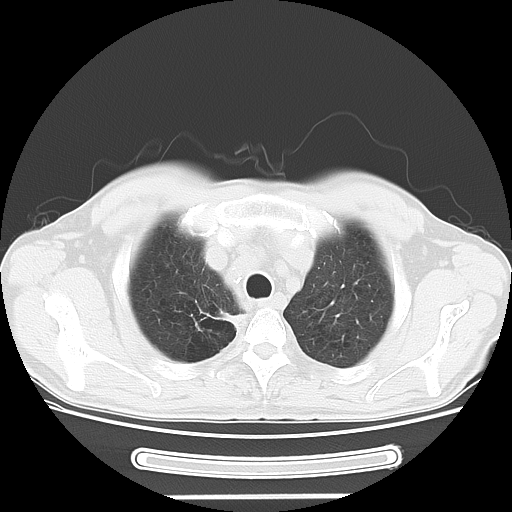
Chest CT, one axial slice. Position 42 of 51 along the scan axis. 120 kVp. Lung window (W 1500 / L -600 HU). 512 × 512 image matrix, field of view 350 × 350 mm. Male patient, age 57 years. From the clinical record (not read from this slice): clinical TNM (as recorded): T2 N3 M1b.
Structures marked on this image (rectangle marked by the reading radiologist):
- lung tumour (recorded histology: adenocarcinoma): bounding box (x1, y1, x2, y2) in pixels: (207, 303, 242, 332)